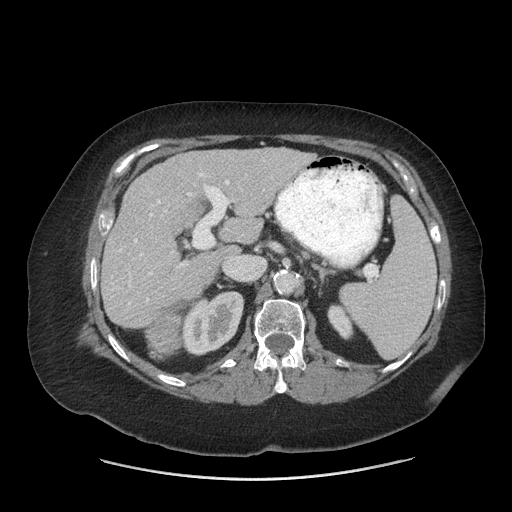
Contrast-enhanced abdominal CT (liver protocol), one axial slice. Position 37 of 69 along the scan axis. Reconstruction kernel STANDARD. 140 kVp. Soft-tissue window (W 400 / L 40 HU). 512 × 512 image matrix. Case-level facts recorded for this patient, not image findings: diagnosis: hepatocellular carcinoma (patient treated with transarterial chemoembolisation; whether this scan precedes or follows treatment is not stated here); TNM stage (as recorded): Stage-IIIB; Child-Pugh class: A; tumour differentiation: moderately differentiated; tumour nodularity: multinodular.
Structures marked on this image (semi-automatically segmented with operator editing):
- liver parenchyma outside the tumour (the mass and vessels are separate outlines, so this box may not span the whole liver): bounding box <102,148,313,326> (left, top, right, bottom; pixels)
- mass: <148,311,178,352>
- liver vessels: <118,173,230,304>